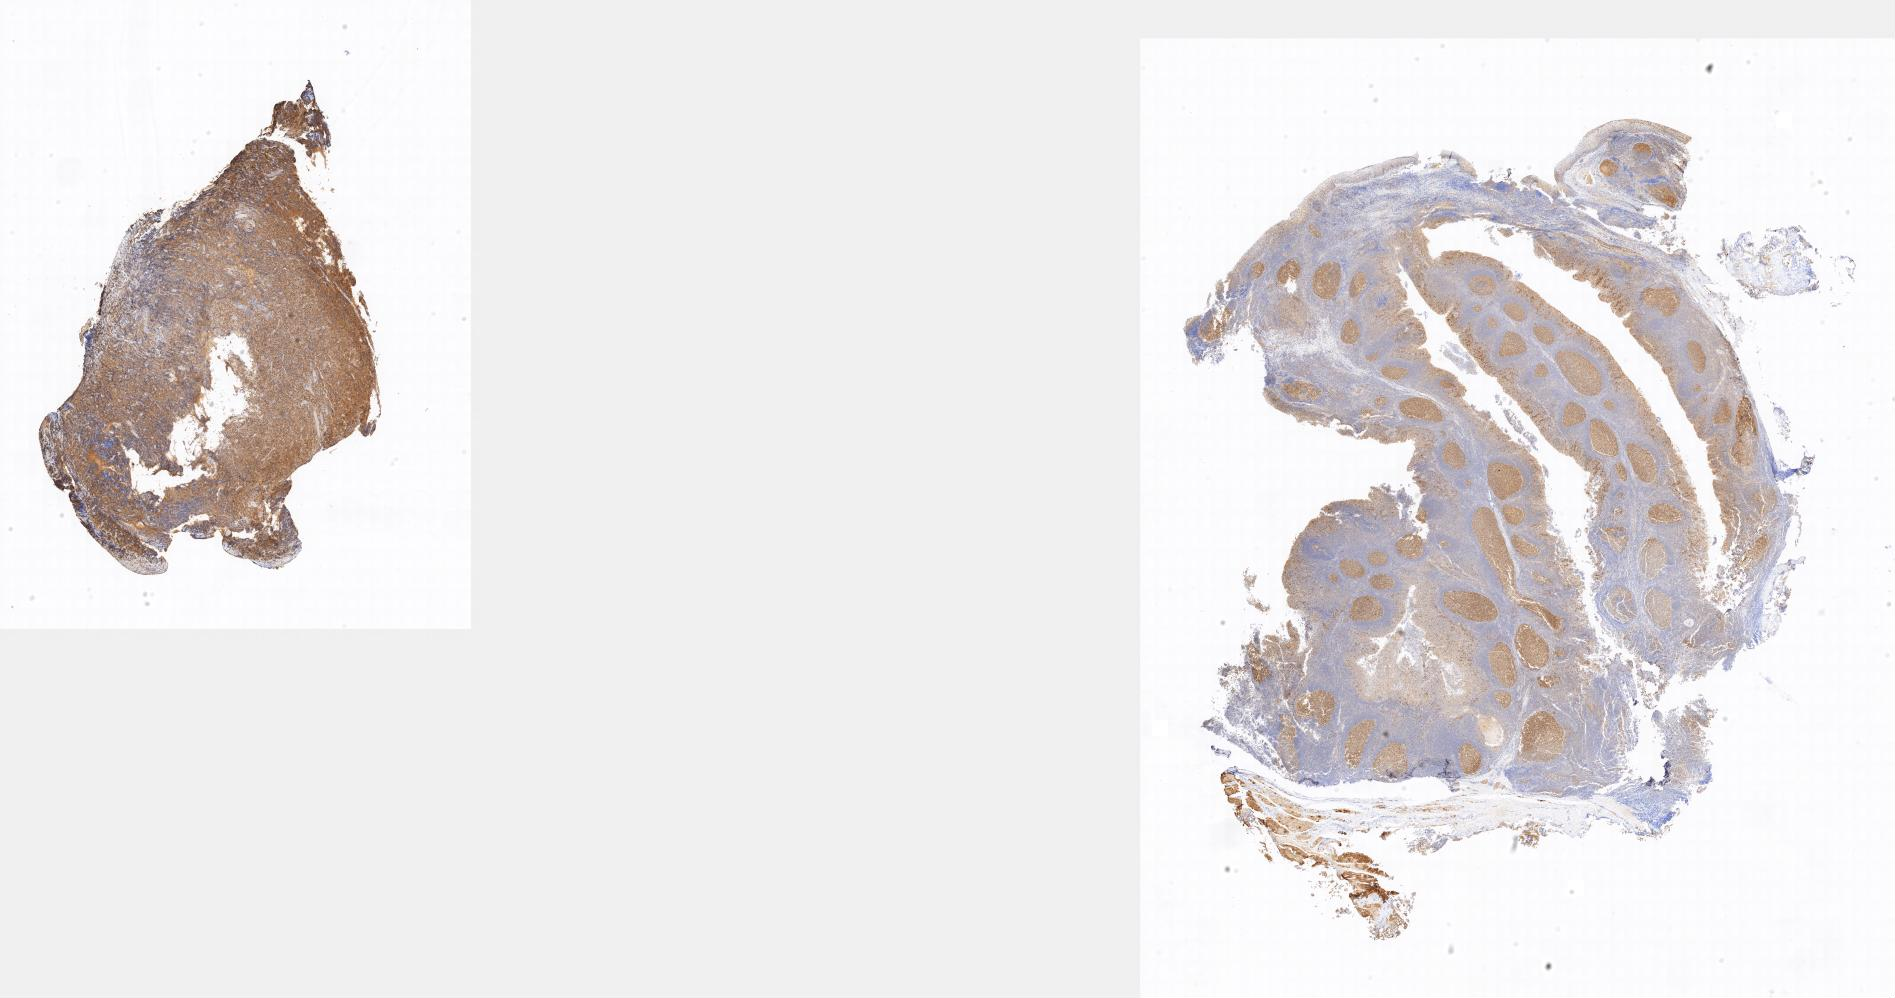
Immunohistochemistry (IHC) whole-slide image stained for BCL6, whole scanned area shown as a low-resolution overview; tumor tissue; site: ovary. Female, age 3 years at initial diagnosis.
Histologic diagnosis: Burkitt lymphoma, NOS.